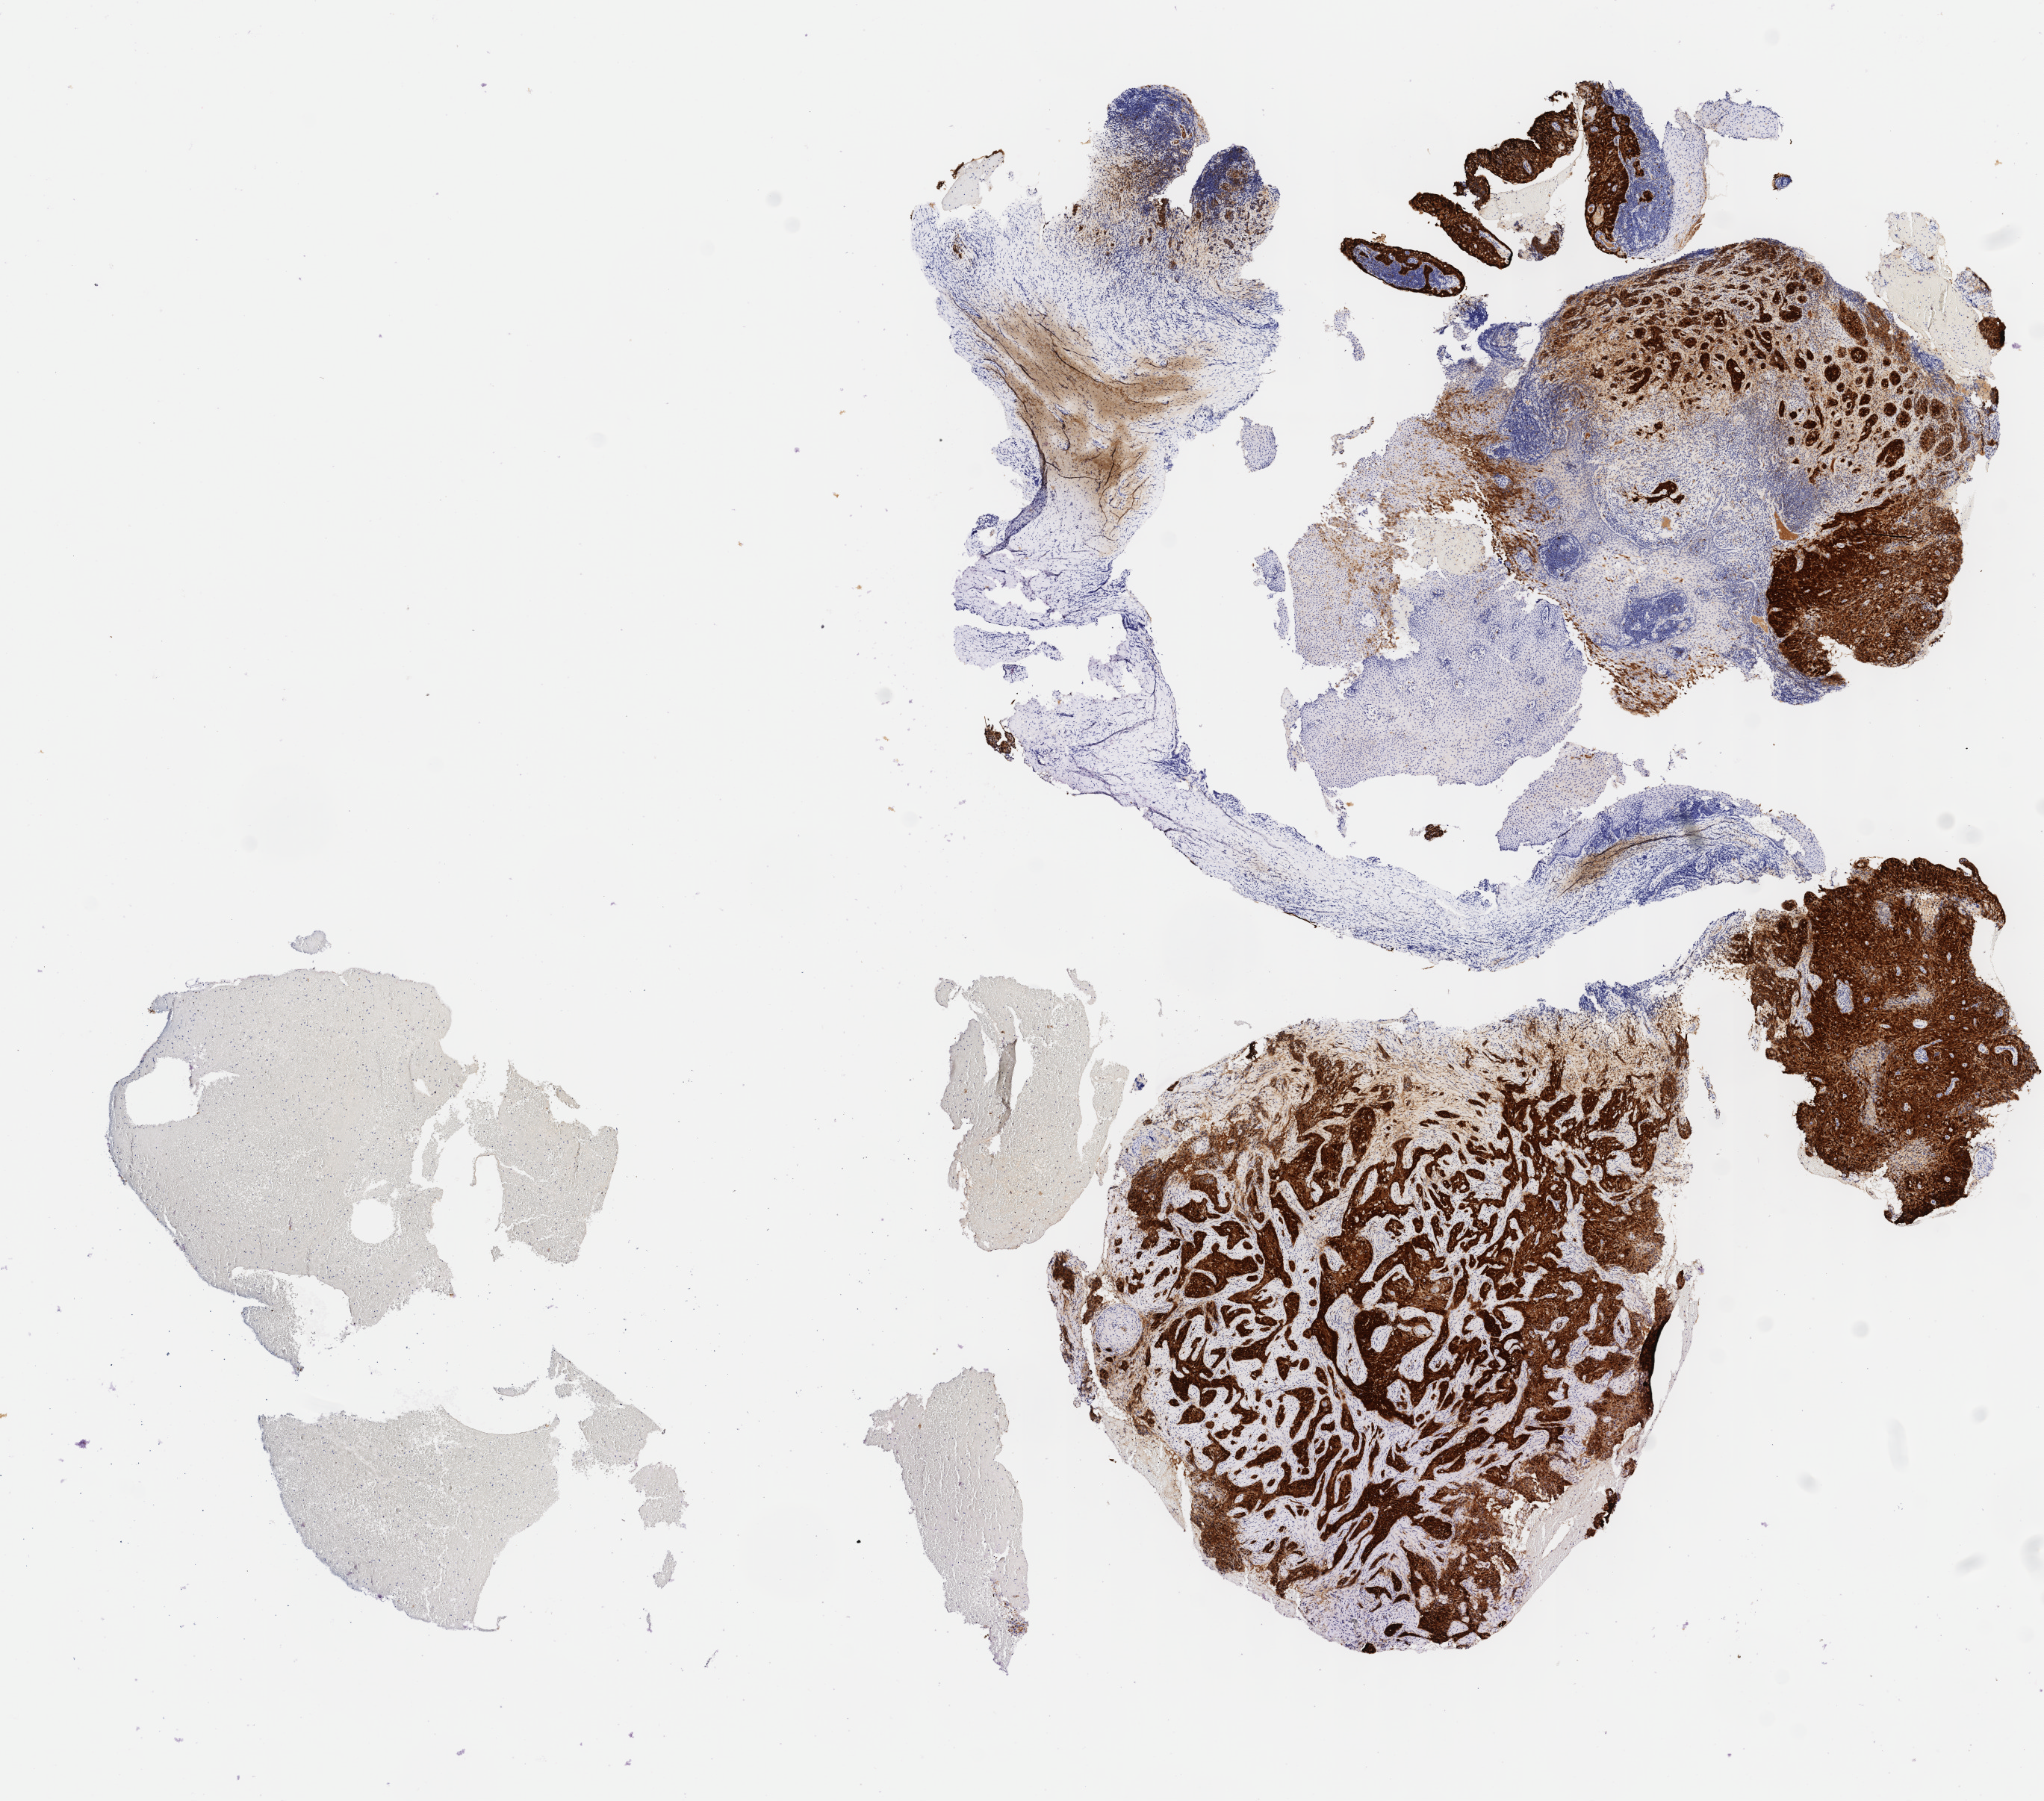
IHC for p16 (p16INK4a), whole-slide image, whole scanned area (about 10.9 x 9.6 mm) shown as a low-resolution overview; specimen: tumor tissue; site: cervix. Female patient, age 47 years.
Diagnosis: Squamous cell carcinoma, large cell, nonkeratinizing, NOS.